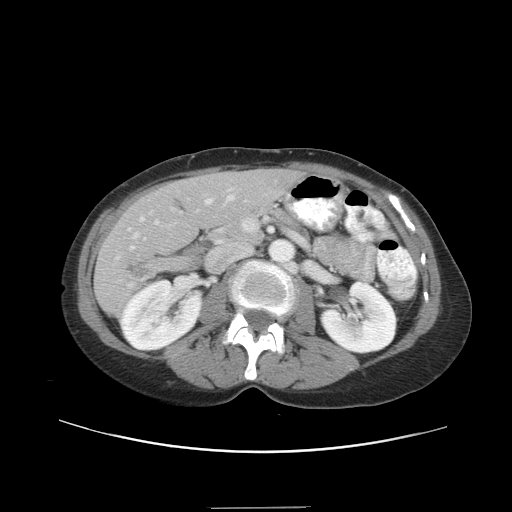
Contrast-enhanced abdominal CT, one axial slice. Slice 16 of 38 in the series (ordered by position). Reconstruction kernel STANDARD. 120 kVp. Intravenous contrast given. Soft-tissue window (W 400 / L 40 HU). 512 × 512 image matrix. Female patient, age 64 years. From the clinical record (not read from this slice): diagnosis: colorectal cancer liver metastases, imaged before liver resection; multiple liver metastases: no; largest metastasis: 3.8 cm; disease in both lobes: yes.
Annotated regions visible in this slice (outlined manually by an expert reader):
- hepatic veins: bounding box <133,195,235,239> (left, top, right, bottom; pixels)
- liver: <96,171,298,314>
- planned liver remnant (the part of the liver to remain after resection): <143,171,298,237>
- portal vein (with intrahepatic branches): <128,189,232,250>
- liver metastasis: <128,263,148,277>